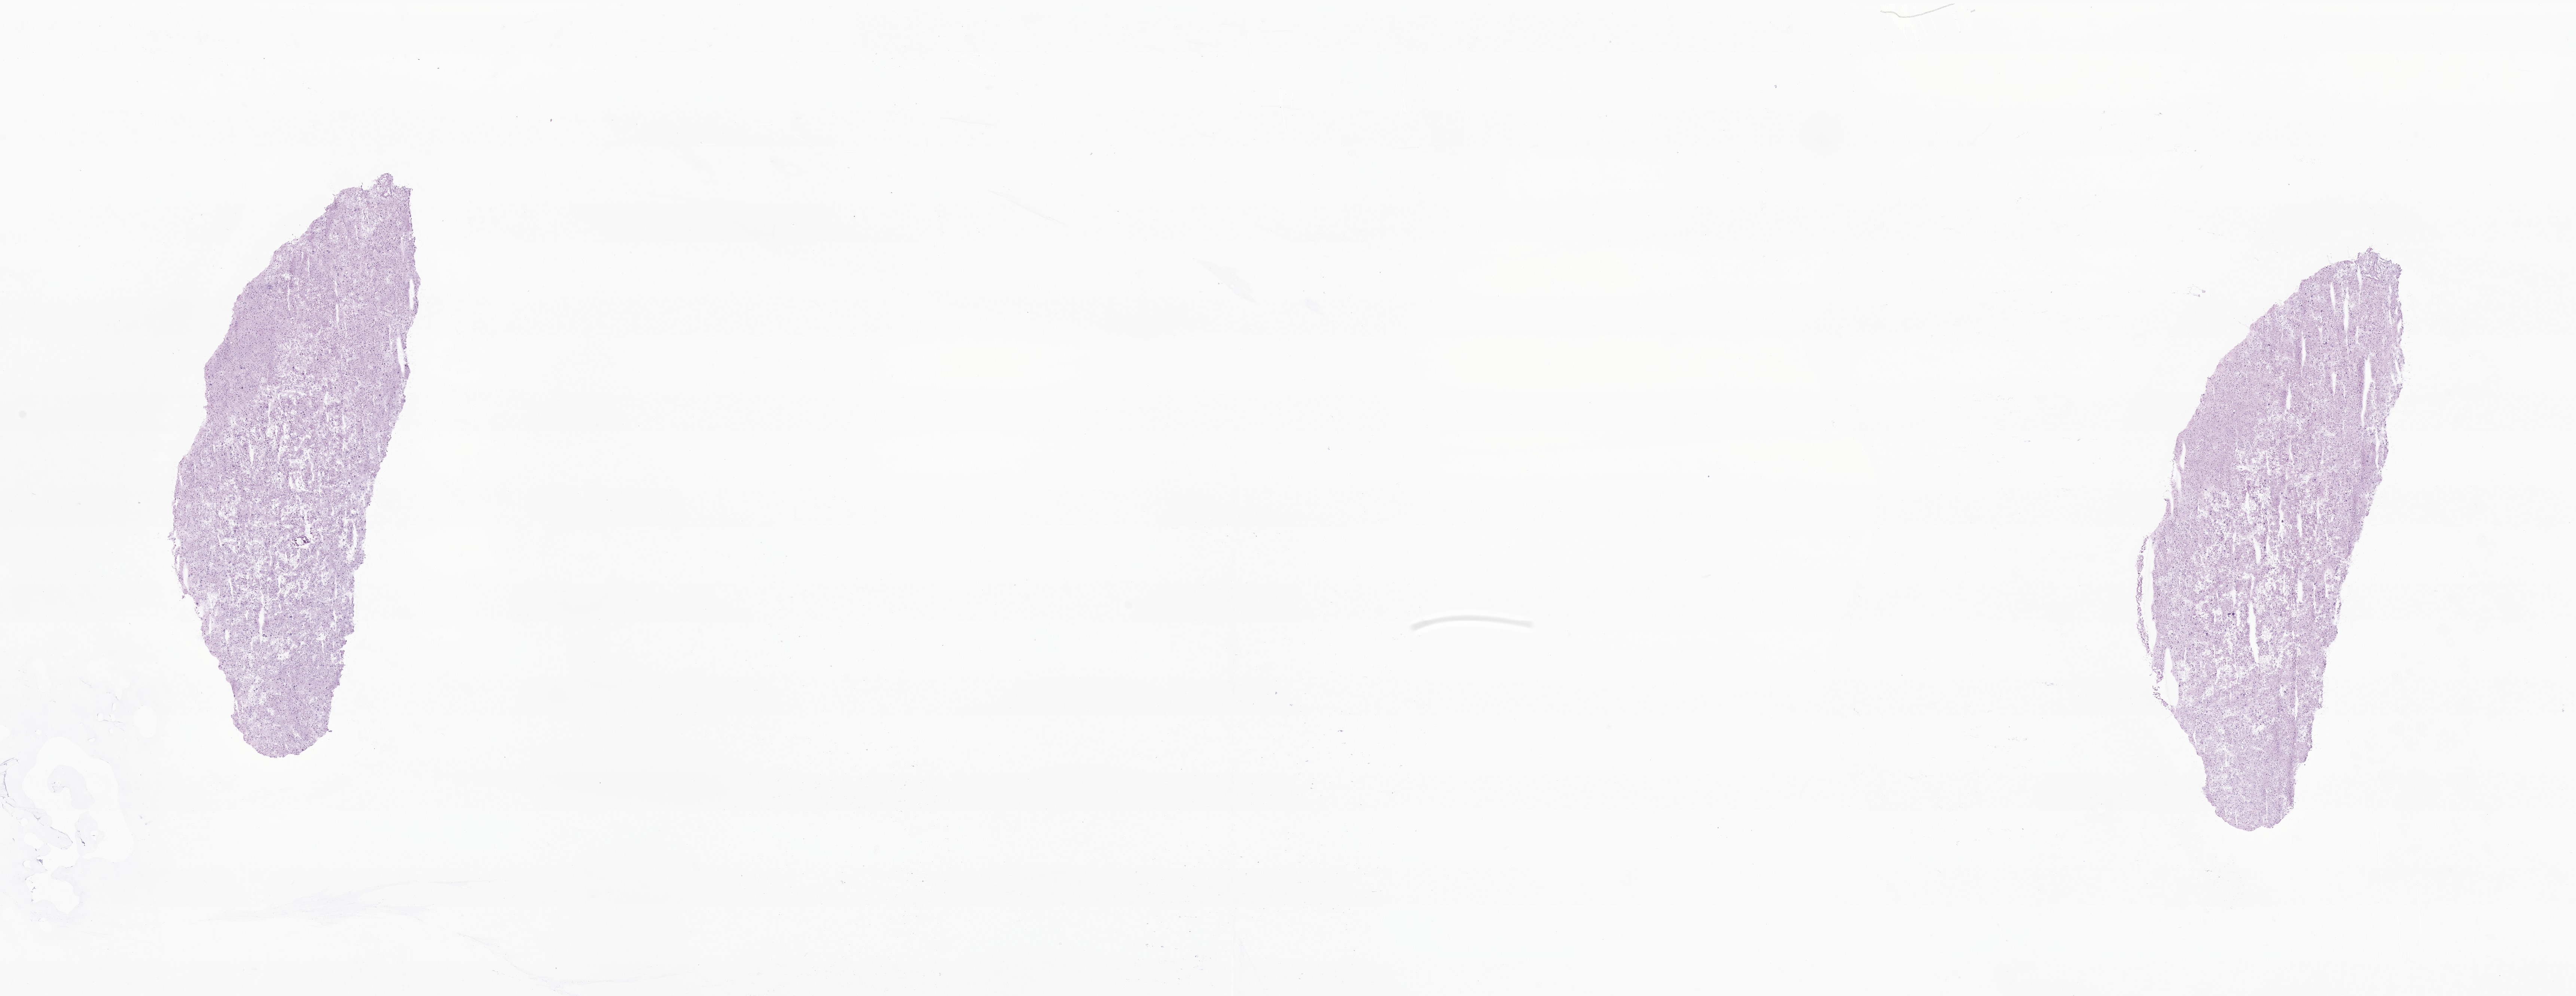
Whole-slide image, haematoxylin and eosin stain of tumor tissue from the adrenal gland, a low-resolution overview of the entire scanned area, about 28.9 x 11.2 mm. Frozen section. Patient female; age 798 days (about 2.2 years).
Recorded diagnosis: Adrenal cortical carcinoma.